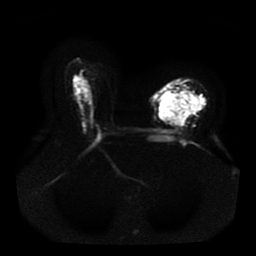
Breast MRI, one axial slice. Position 27 of 41 along the scan axis. Diffusion-weighted series; image 2 of 4 stored at this slice position (different b-values; order by instance number). 1.5 T. 5 mm slice thickness. 256 × 256 image matrix, field of view 330 × 330 mm. Female patient.
Outlined on this slice (manually delineated by an expert):
- tumour on diffusion-weighted imaging: bounding box (x1, y1, x2, y2) in pixels: (160, 92, 205, 124)